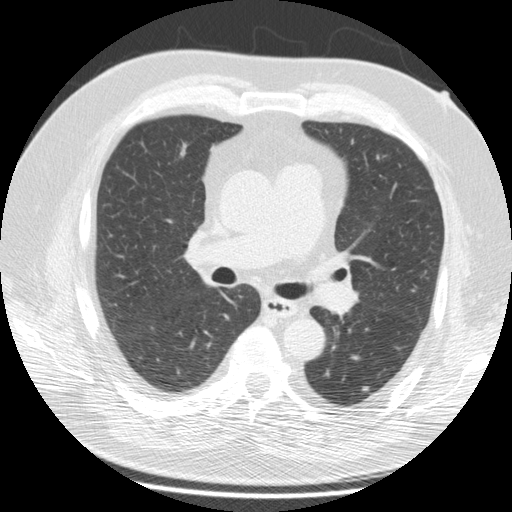
Low-dose screening chest CT, one axial slice; reconstruction kernel STANDARD; 120 kVp; lung window (W 1500 / L -600 HU); 512 × 512 image matrix, field of view 364 × 364 mm.
Outlined on this slice (outlined manually by an expert reader):
- lesion 1 (tumor, lower lobe of left lung): bounding box <362,386,369,392> (left, top, right, bottom; pixels)